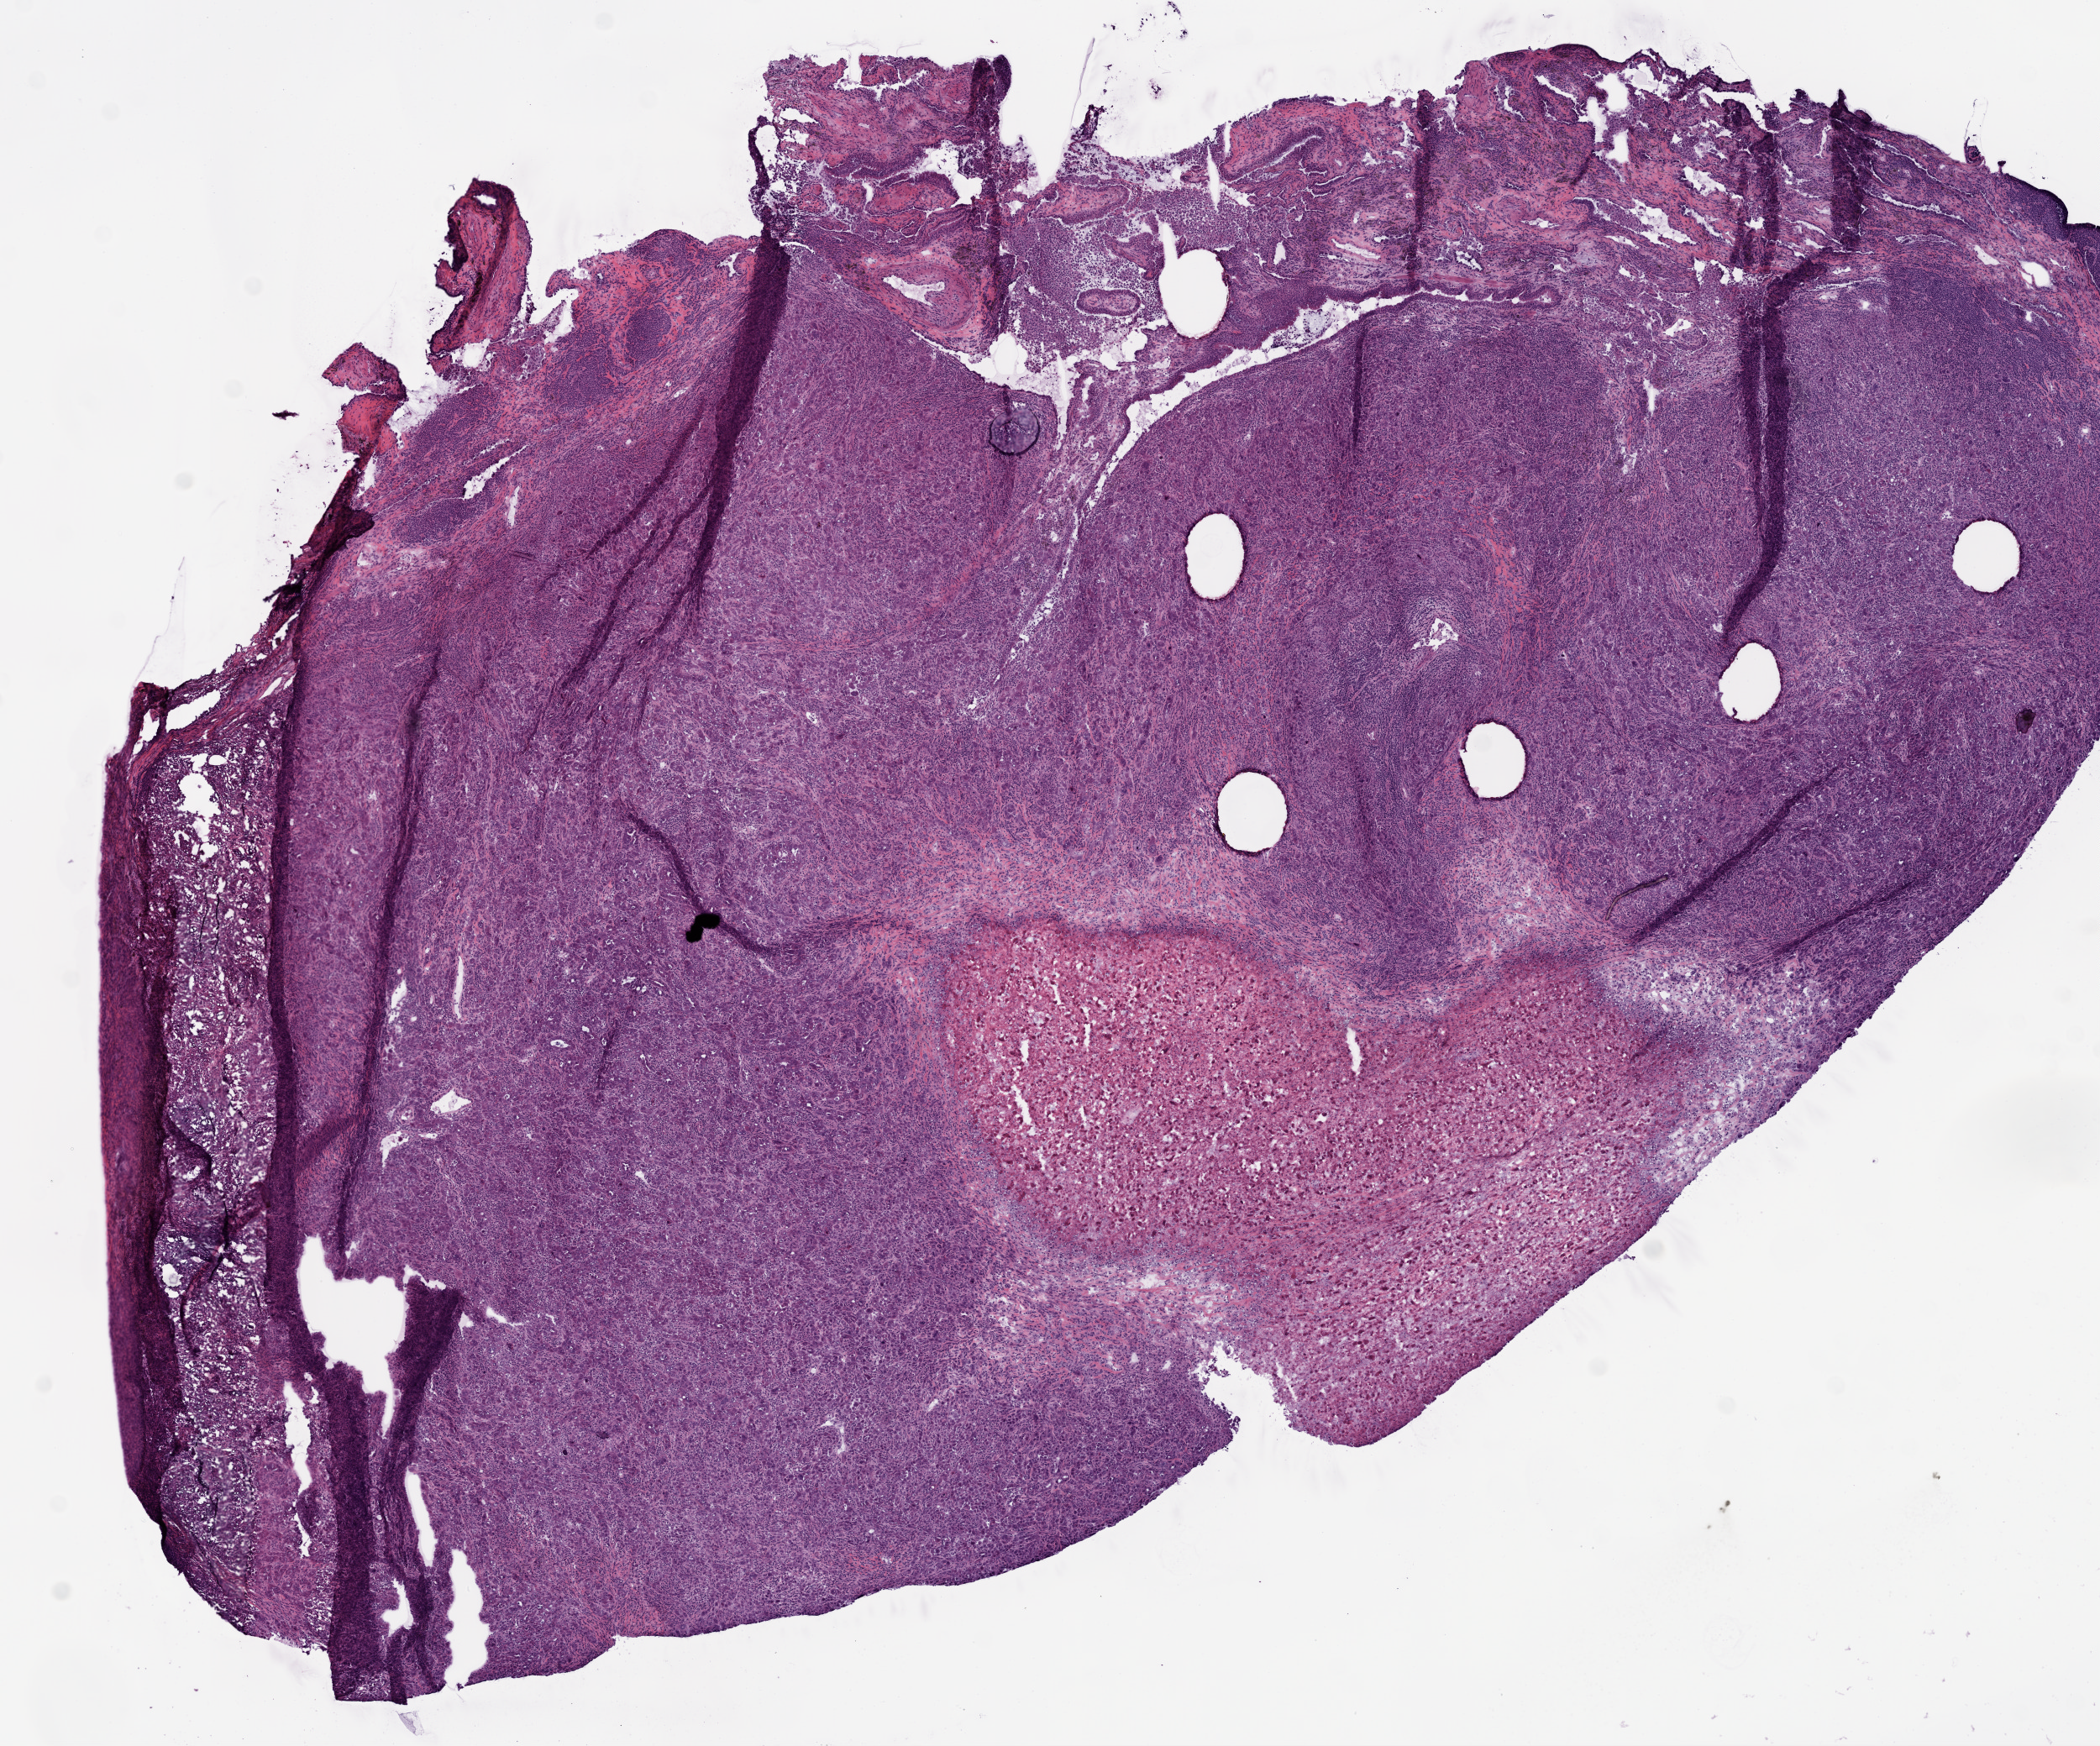
H&E whole-slide image, a low-resolution overview of the entire scanned area, about 10.0 x 8.3 mm; frozen section from the top of the tissue portion; sample: primary tumour, lung. Male, age 71 years at initial diagnosis. Slide review estimates, as recorded: tumour cells 100%, tumour nuclei 61%, normal cells 0%, stromal cells 0%, necrosis 0%. Infiltration values recorded for this section: lymphocyte infiltration 25%.
TNM: T1a N0 M0. Laterality: left. AJCC pathologic stage: IA (7th edition). Diagnosis: Adenocarcinoma, NOS (lower lobe, lung).